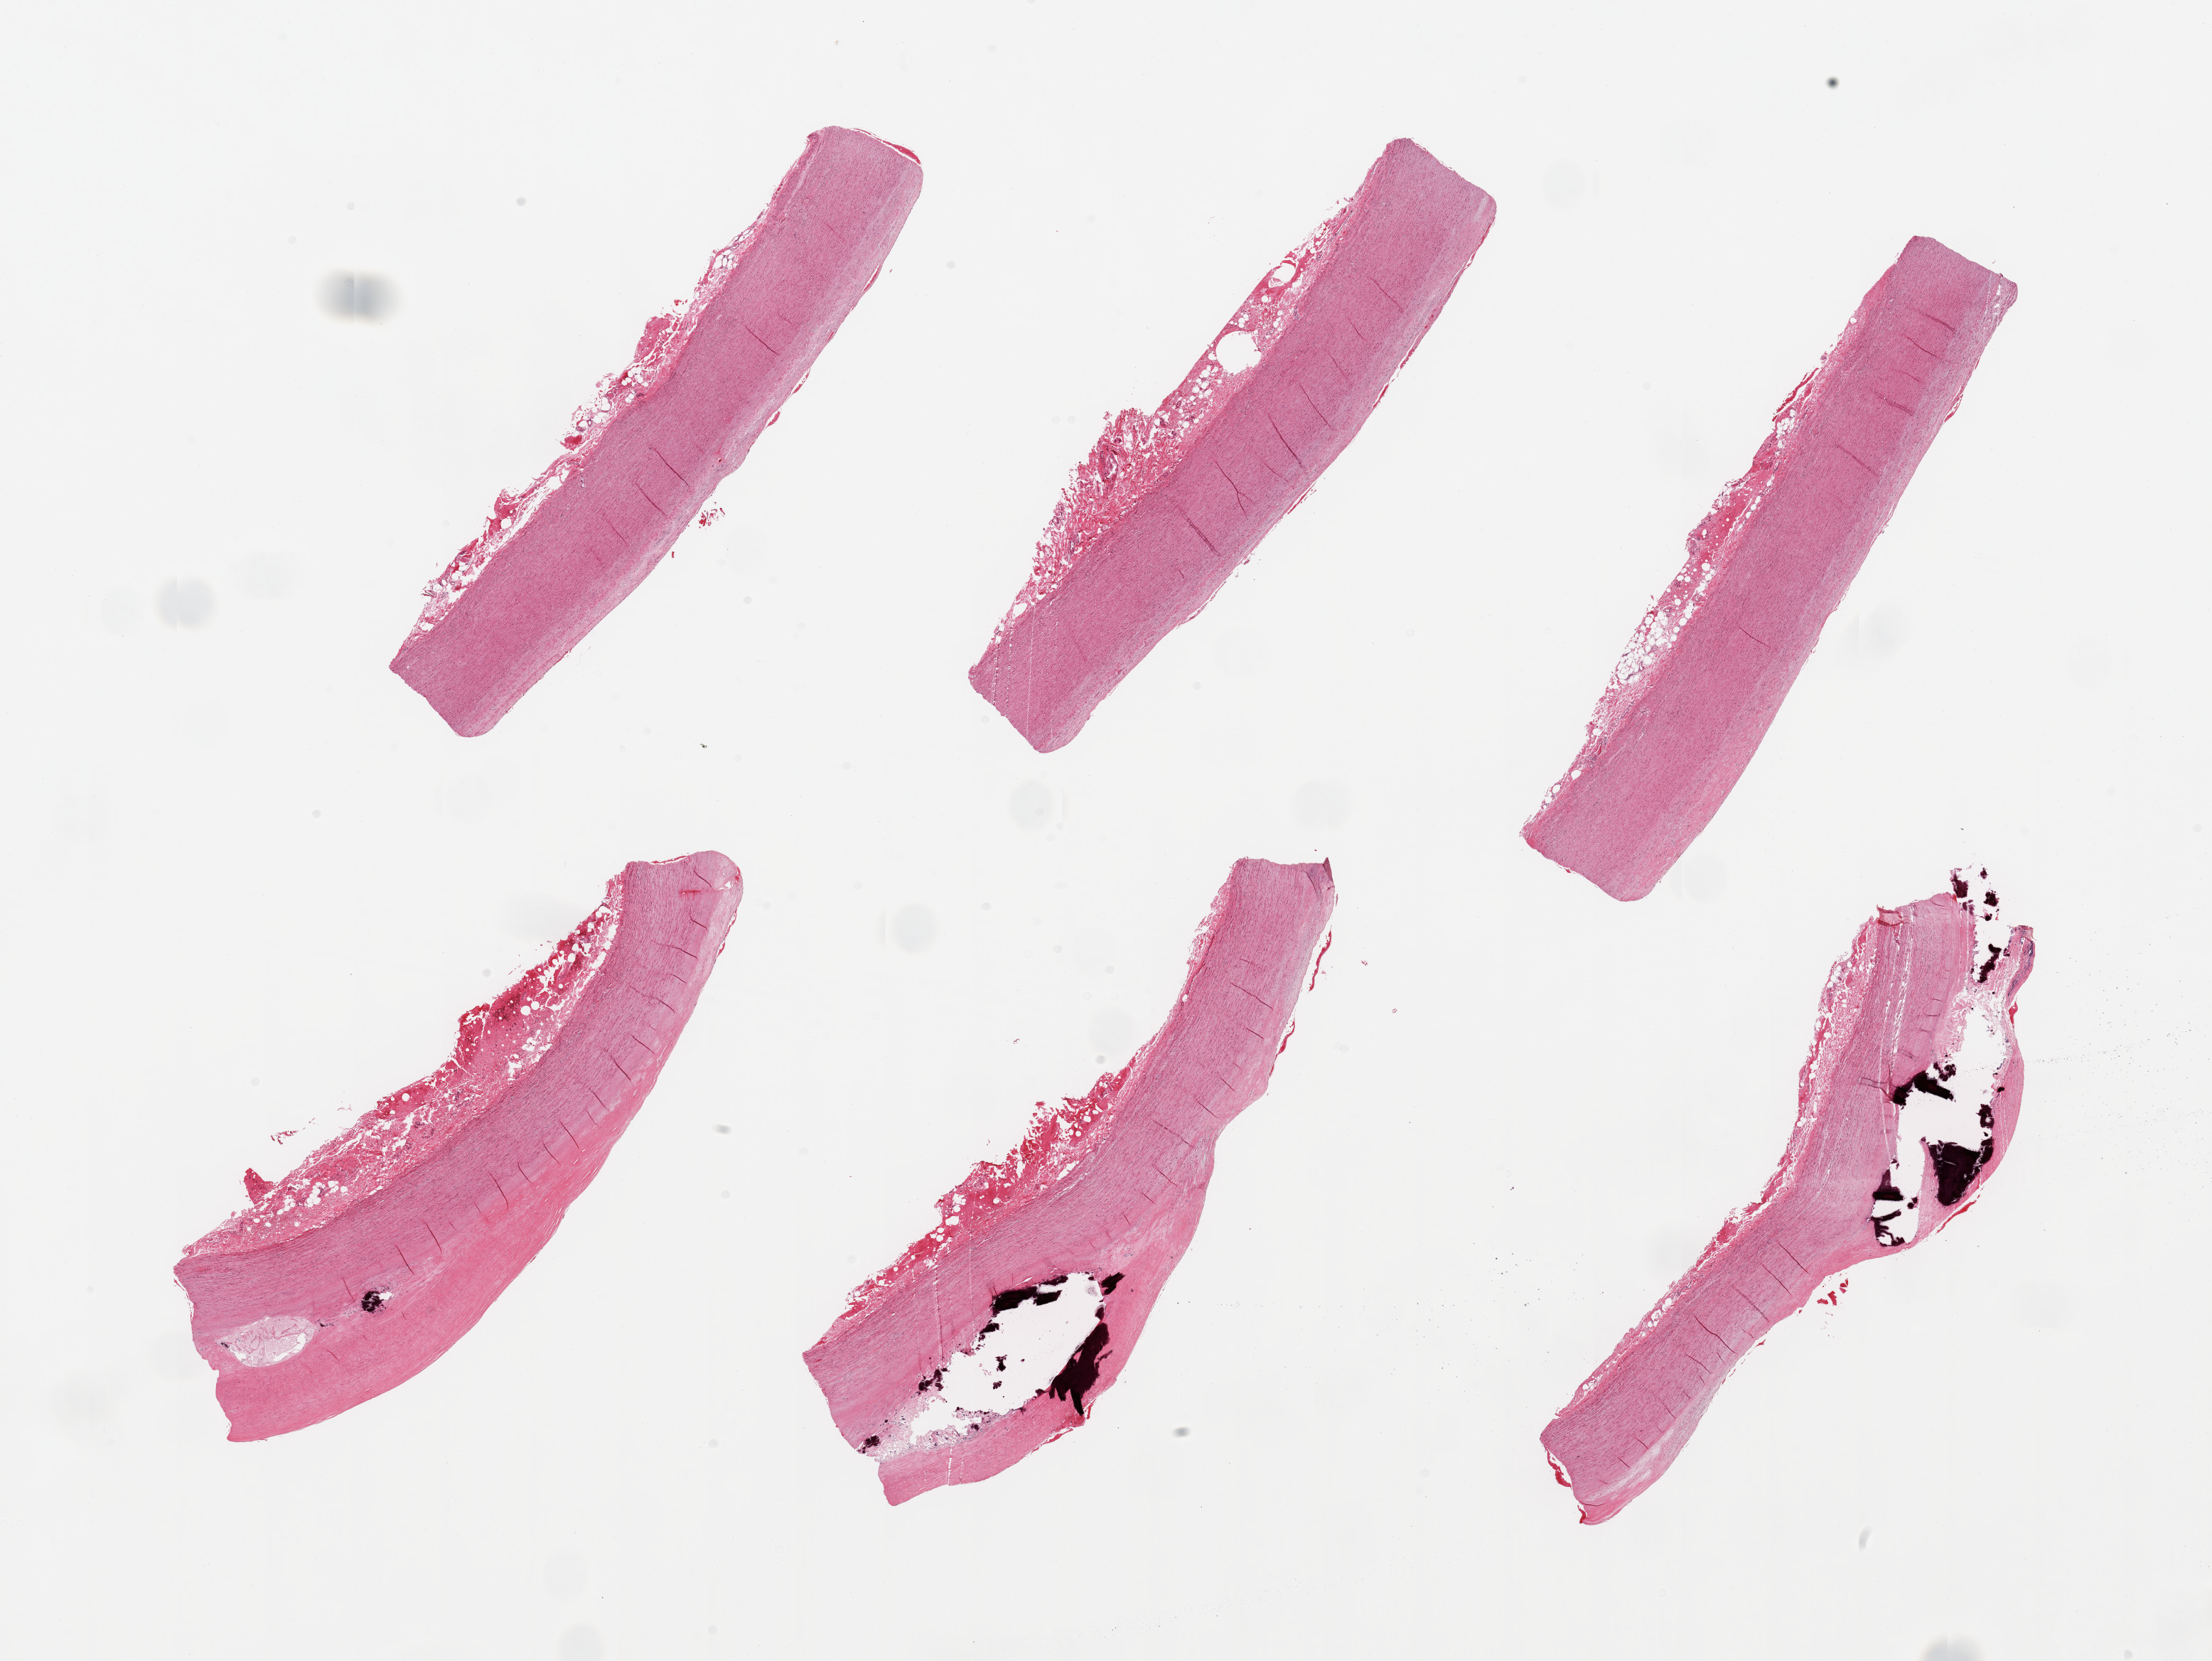
Digitized H&E-stained section — low-resolution overview of the scanned area, about 24.6 x 18.5 mm (from a 20x scan). PAXgene-fixed paraffin-embedded (PFPE) section. Sampled site (target tissue): aorta. Donor tissue sample. Male donor.
Review note (as recorded): 6 pieces; atheromatous change with calcification.